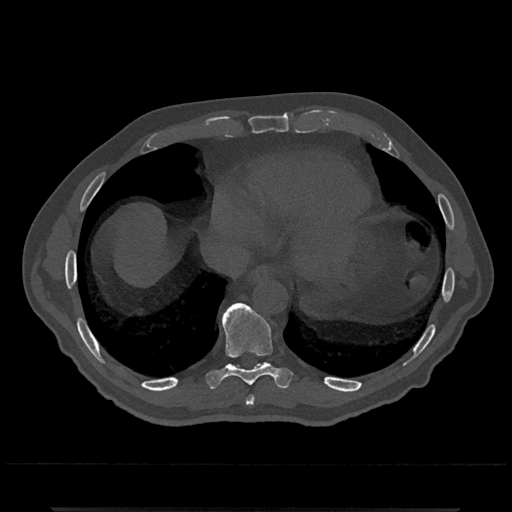
CT including the spine, one axial slice; reconstruction kernel Br40s/3; bone window (W 1800 / L 400 HU); 0.5 mm slice thickness; 512 × 512 image matrix, field of view 393 × 393 mm. Male patient, age 67 years. From the clinical record (not read from this slice): primary cancer: prostate.
Outlined on this slice (semi-automatically segmented with operator editing):
- T8 vertebra: bounding box (x1, y1, x2, y2) in pixels: (246, 396, 255, 405)
- T9 vertebra: (206, 302, 293, 388)